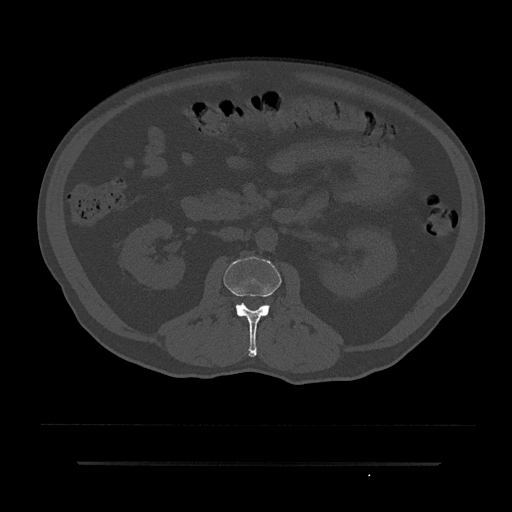
CT including the spine, one axial slice; position 63 of 797 along the scan axis; reconstruction kernel Br40s/3; 120 kVp; bone window (W 1800 / L 400 HU); 512 × 512 image matrix, field of view 464 × 464 mm. Male patient, age 59 years. Case-level facts recorded for this patient, not image findings: primary cancer: bile ducts.
Structures marked on this image (semi-automatically segmented with operator editing):
- L2 vertebra: bounding box (x1, y1, x2, y2) in pixels: (224, 257, 281, 357)